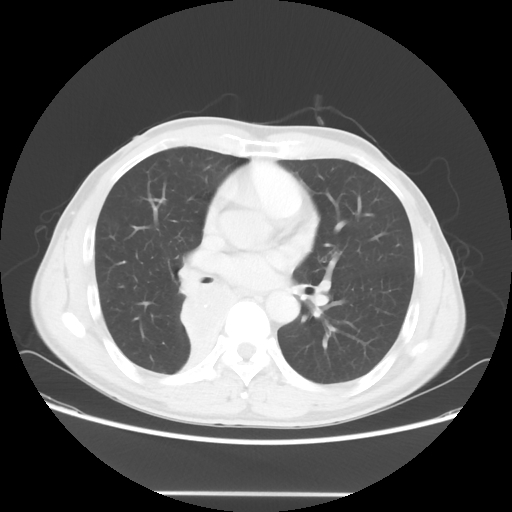
Chest CT, one axial slice; slice 32 of 62 in the series (ordered by position); 120 kVp; lung window (W 1500 / L -600 HU); 5 mm slice thickness; 512 × 512 image matrix. Patient: male, 47 years. From the clinical record (not read from this slice): clinical TNM (as recorded): T2 N0 M0.
Outlined on this slice (bounding box drawn by a radiologist):
- lung tumour (recorded histology: squamous cell carcinoma): bounding box (x1, y1, x2, y2) in pixels: (176, 274, 244, 356)